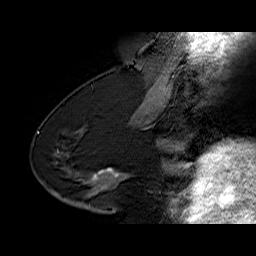
Breast MRI (dynamic contrast-enhanced), one sagittal slice. Dynamic contrast-enhanced series, time point 2 of 6 at this slice position (early post-contrast). 1.5 T. TE 6.4 ms, TR 32.9 ms. 256 × 256 image matrix, field of view 200 × 200 mm. Female patient. From the clinical record (not read from this slice): setting: breast cancer imaged before/during neoadjuvant chemotherapy; receptor status: HR-positive, HER2-negative.
Annotated regions visible in this slice (semi-automatically segmented with operator editing):
- analysis volume of interest (the breast-tissue region the enhancement analysis was run in; not a lesion): box from (x=68, y=154) to (x=129, y=203) px
- tumour enhancement mask (voxels above the 100 % enhancement threshold inside the analysis volume of interest): (x=91, y=168)–(x=127, y=184)